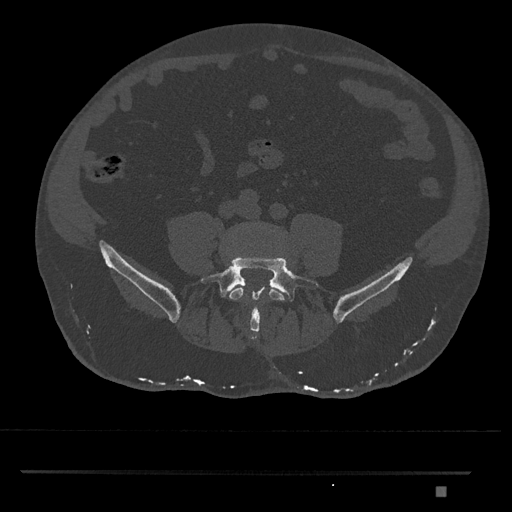
CT including the spine, one axial slice. Position 575 of 1134 along the scan axis. Reconstruction kernel Br40s/3. 120 kVp. Bone window (W 1800 / L 400 HU). 0.5 mm slice thickness. 512 × 512 image matrix. Male patient, age 65 years. Case-level facts recorded for this patient, not image findings: primary cancer: prostate.
Outlined on this slice (semi-automatic segmentation, software-assisted and operator-edited):
- L4 vertebra: bounding box <229,222,285,302> (left, top, right, bottom; pixels)
- L5 vertebra: <201,255,322,334>